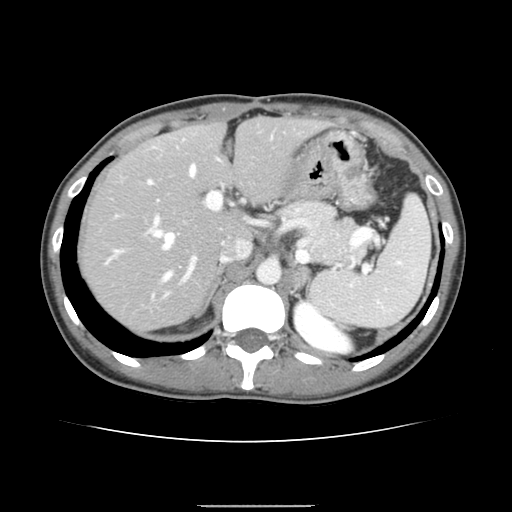
Contrast-enhanced abdominal CT, one axial slice; slice 101 of 150 in the series (ordered by position); soft-tissue window (W 400 / L 40 HU); 2.5 mm slice thickness; 512 × 512 image matrix, field of view 324 × 324 mm. Female patient, age 32 years. From the clinical record (not read from this slice): diagnosis: colorectal cancer liver metastases, imaged before liver resection; multiple liver metastases: yes; largest metastasis: 0.7 cm.
Structures marked on this image (expert manual segmentation):
- hepatic veins: bounding box [x1, y1, x2, y2] px = [115, 165, 195, 279]
- liver: [82, 118, 318, 330]
- planned liver remnant (the part of the liver to remain after resection): [82, 118, 320, 281]
- portal vein (with intrahepatic branches): [106, 139, 222, 295]